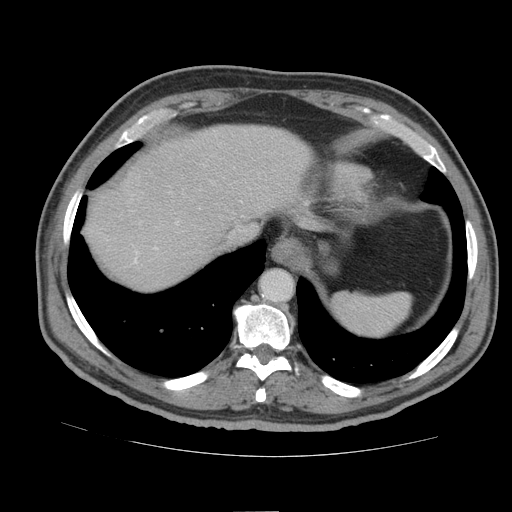
Contrast-enhanced abdominal CT (liver protocol), one axial slice; reconstruction kernel STANDARD; soft-tissue window (W 400 / L 40 HU); 2.5 mm slice thickness; 512 × 512 image matrix, field of view 380 × 380 mm. From the clinical record (not read from this slice): diagnosis: hepatocellular carcinoma (patient treated with transarterial chemoembolisation; whether this scan precedes or follows treatment is not stated here); TNM stage (as recorded): Stage-IIIB; Child-Pugh class: A.
Annotated regions visible in this slice (semi-automatically segmented with operator editing):
- abdominal aorta: bounding box (x1, y1, x2, y2) in pixels: (261, 271, 293, 301)
- liver parenchyma outside the tumour (the mass and vessels are separate outlines, so this box may not span the whole liver): (86, 124, 313, 290)
- liver vessels: (135, 248, 157, 263)